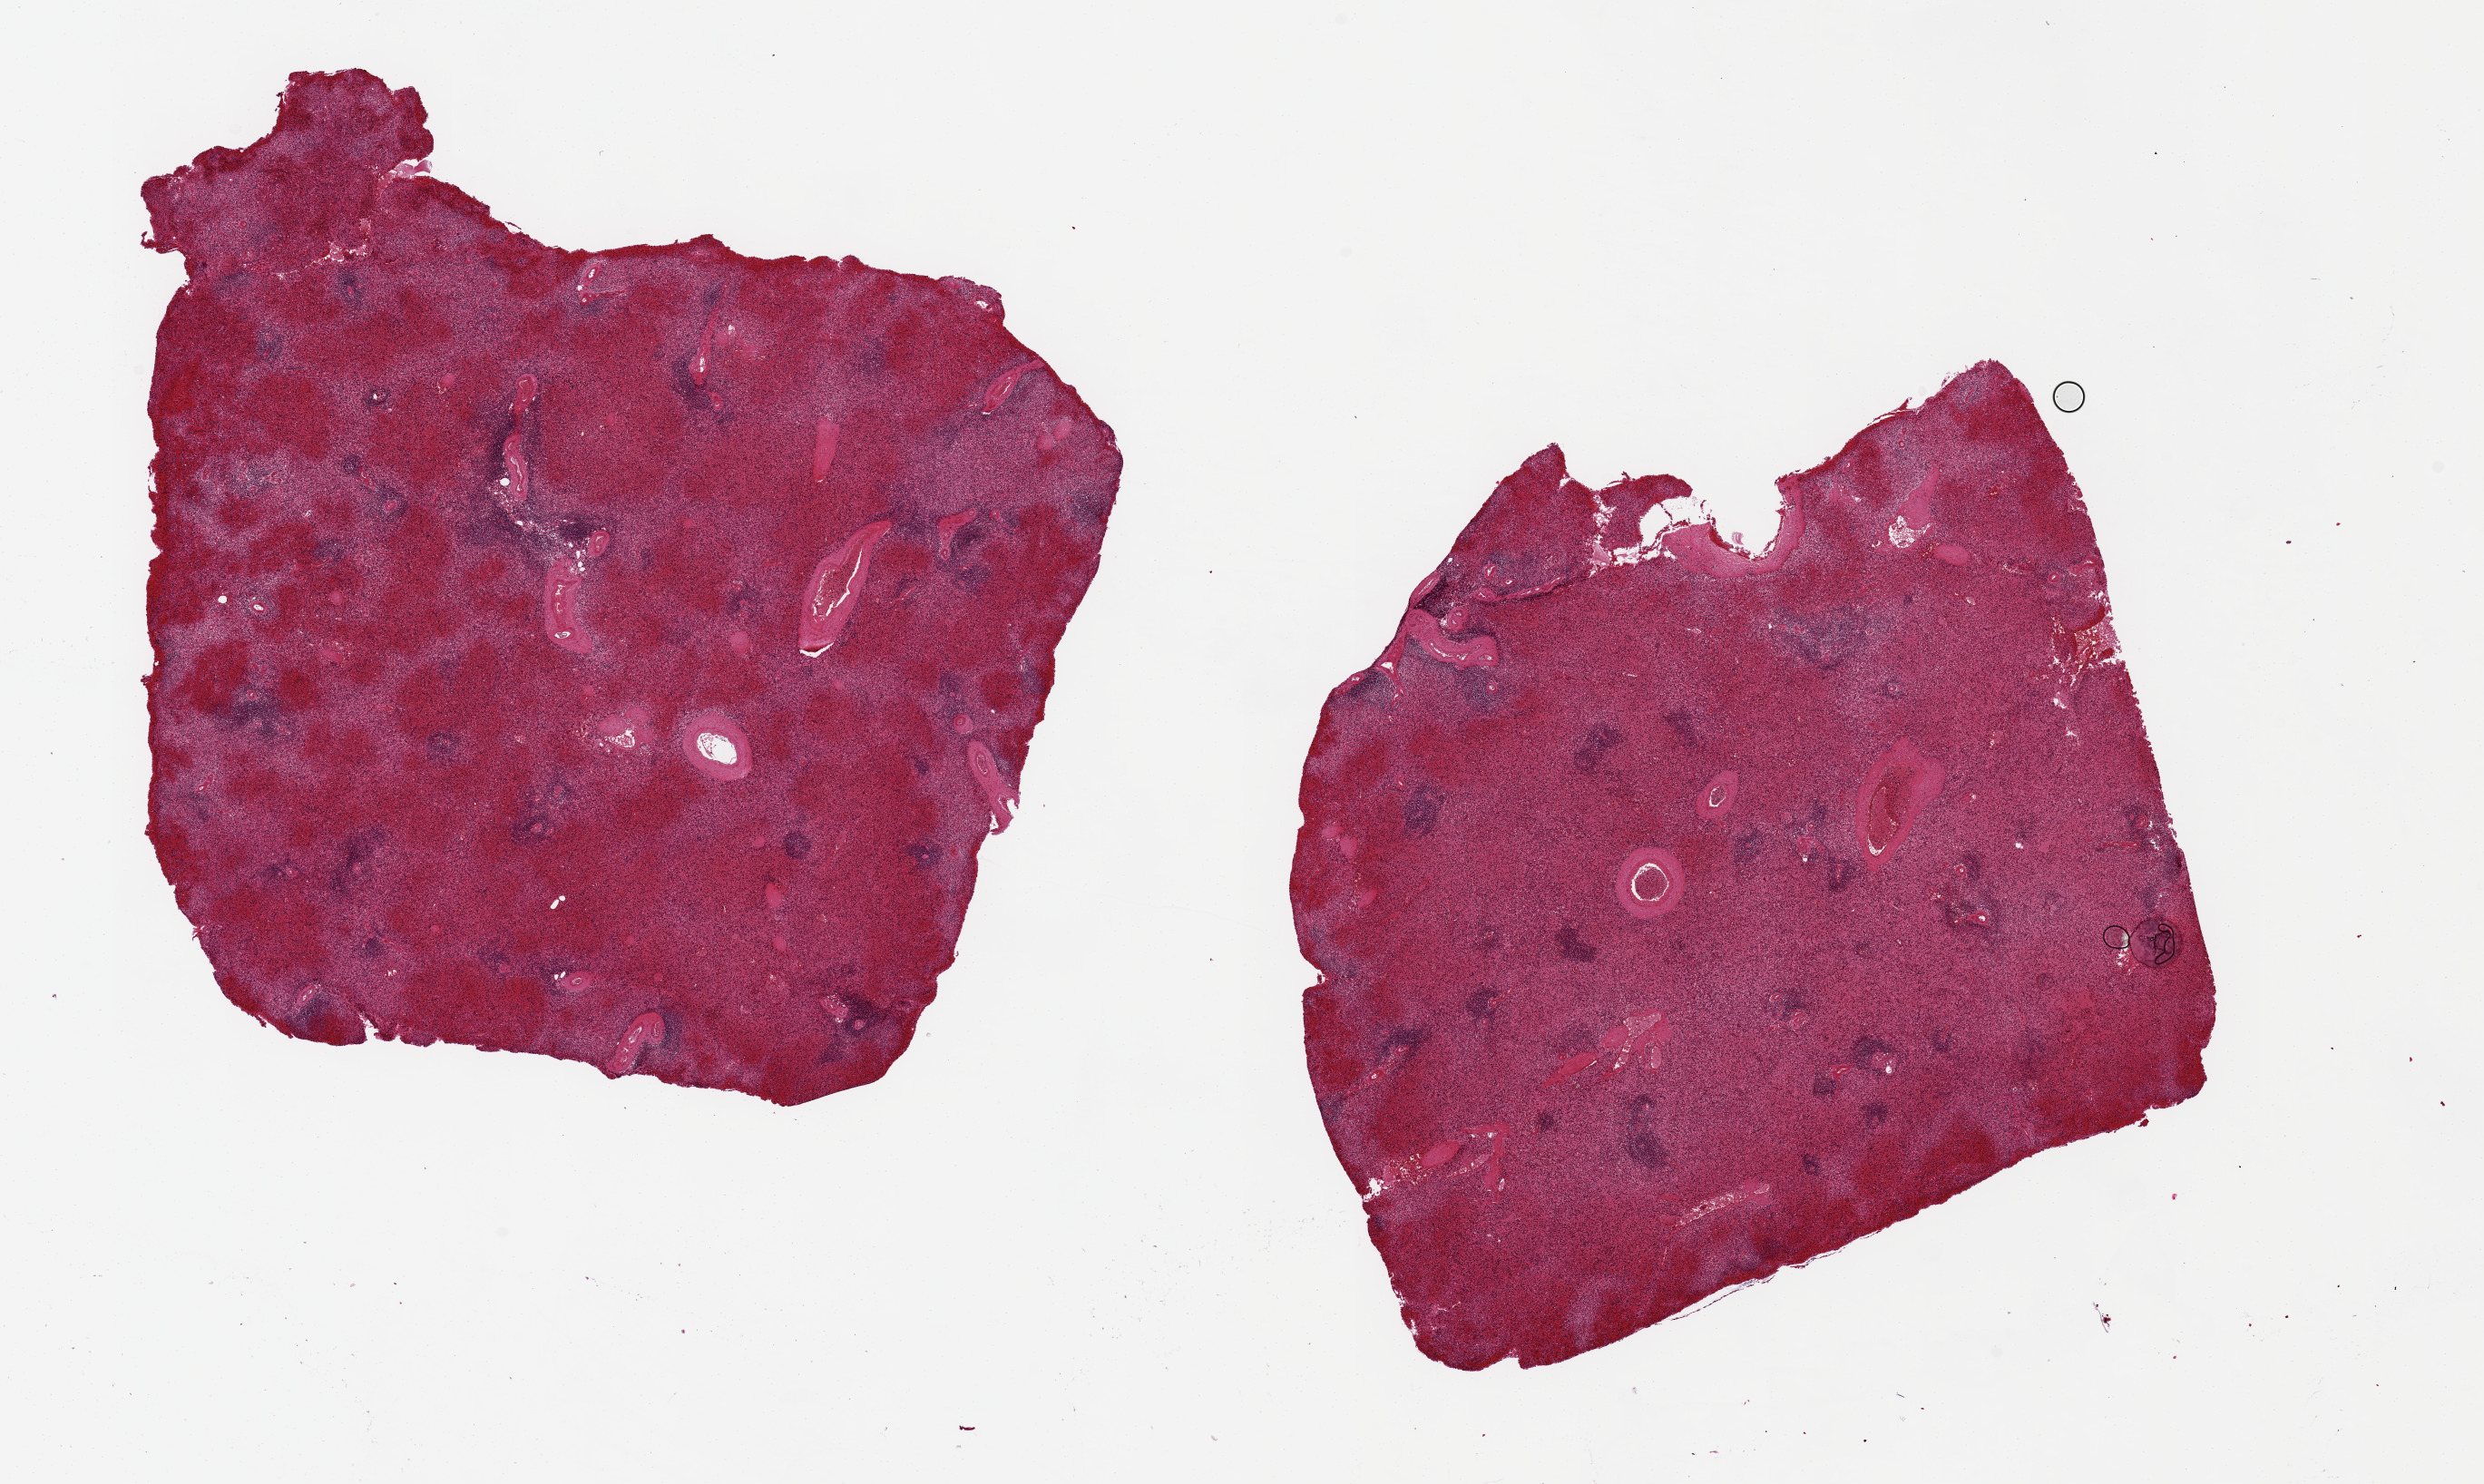
Haematoxylin and eosin whole-slide image, whole scanned area (about 21.7 x 12.9 mm, acquisition: 20x scan) shown as a low-resolution overview, PAXgene-fixed, paraffin-embedded tissue, sampled site (target tissue): spleen, donor tissue sample.
* reviewer comment on this tissue sample: 2 pieces, both 8x7mm; marked congestion